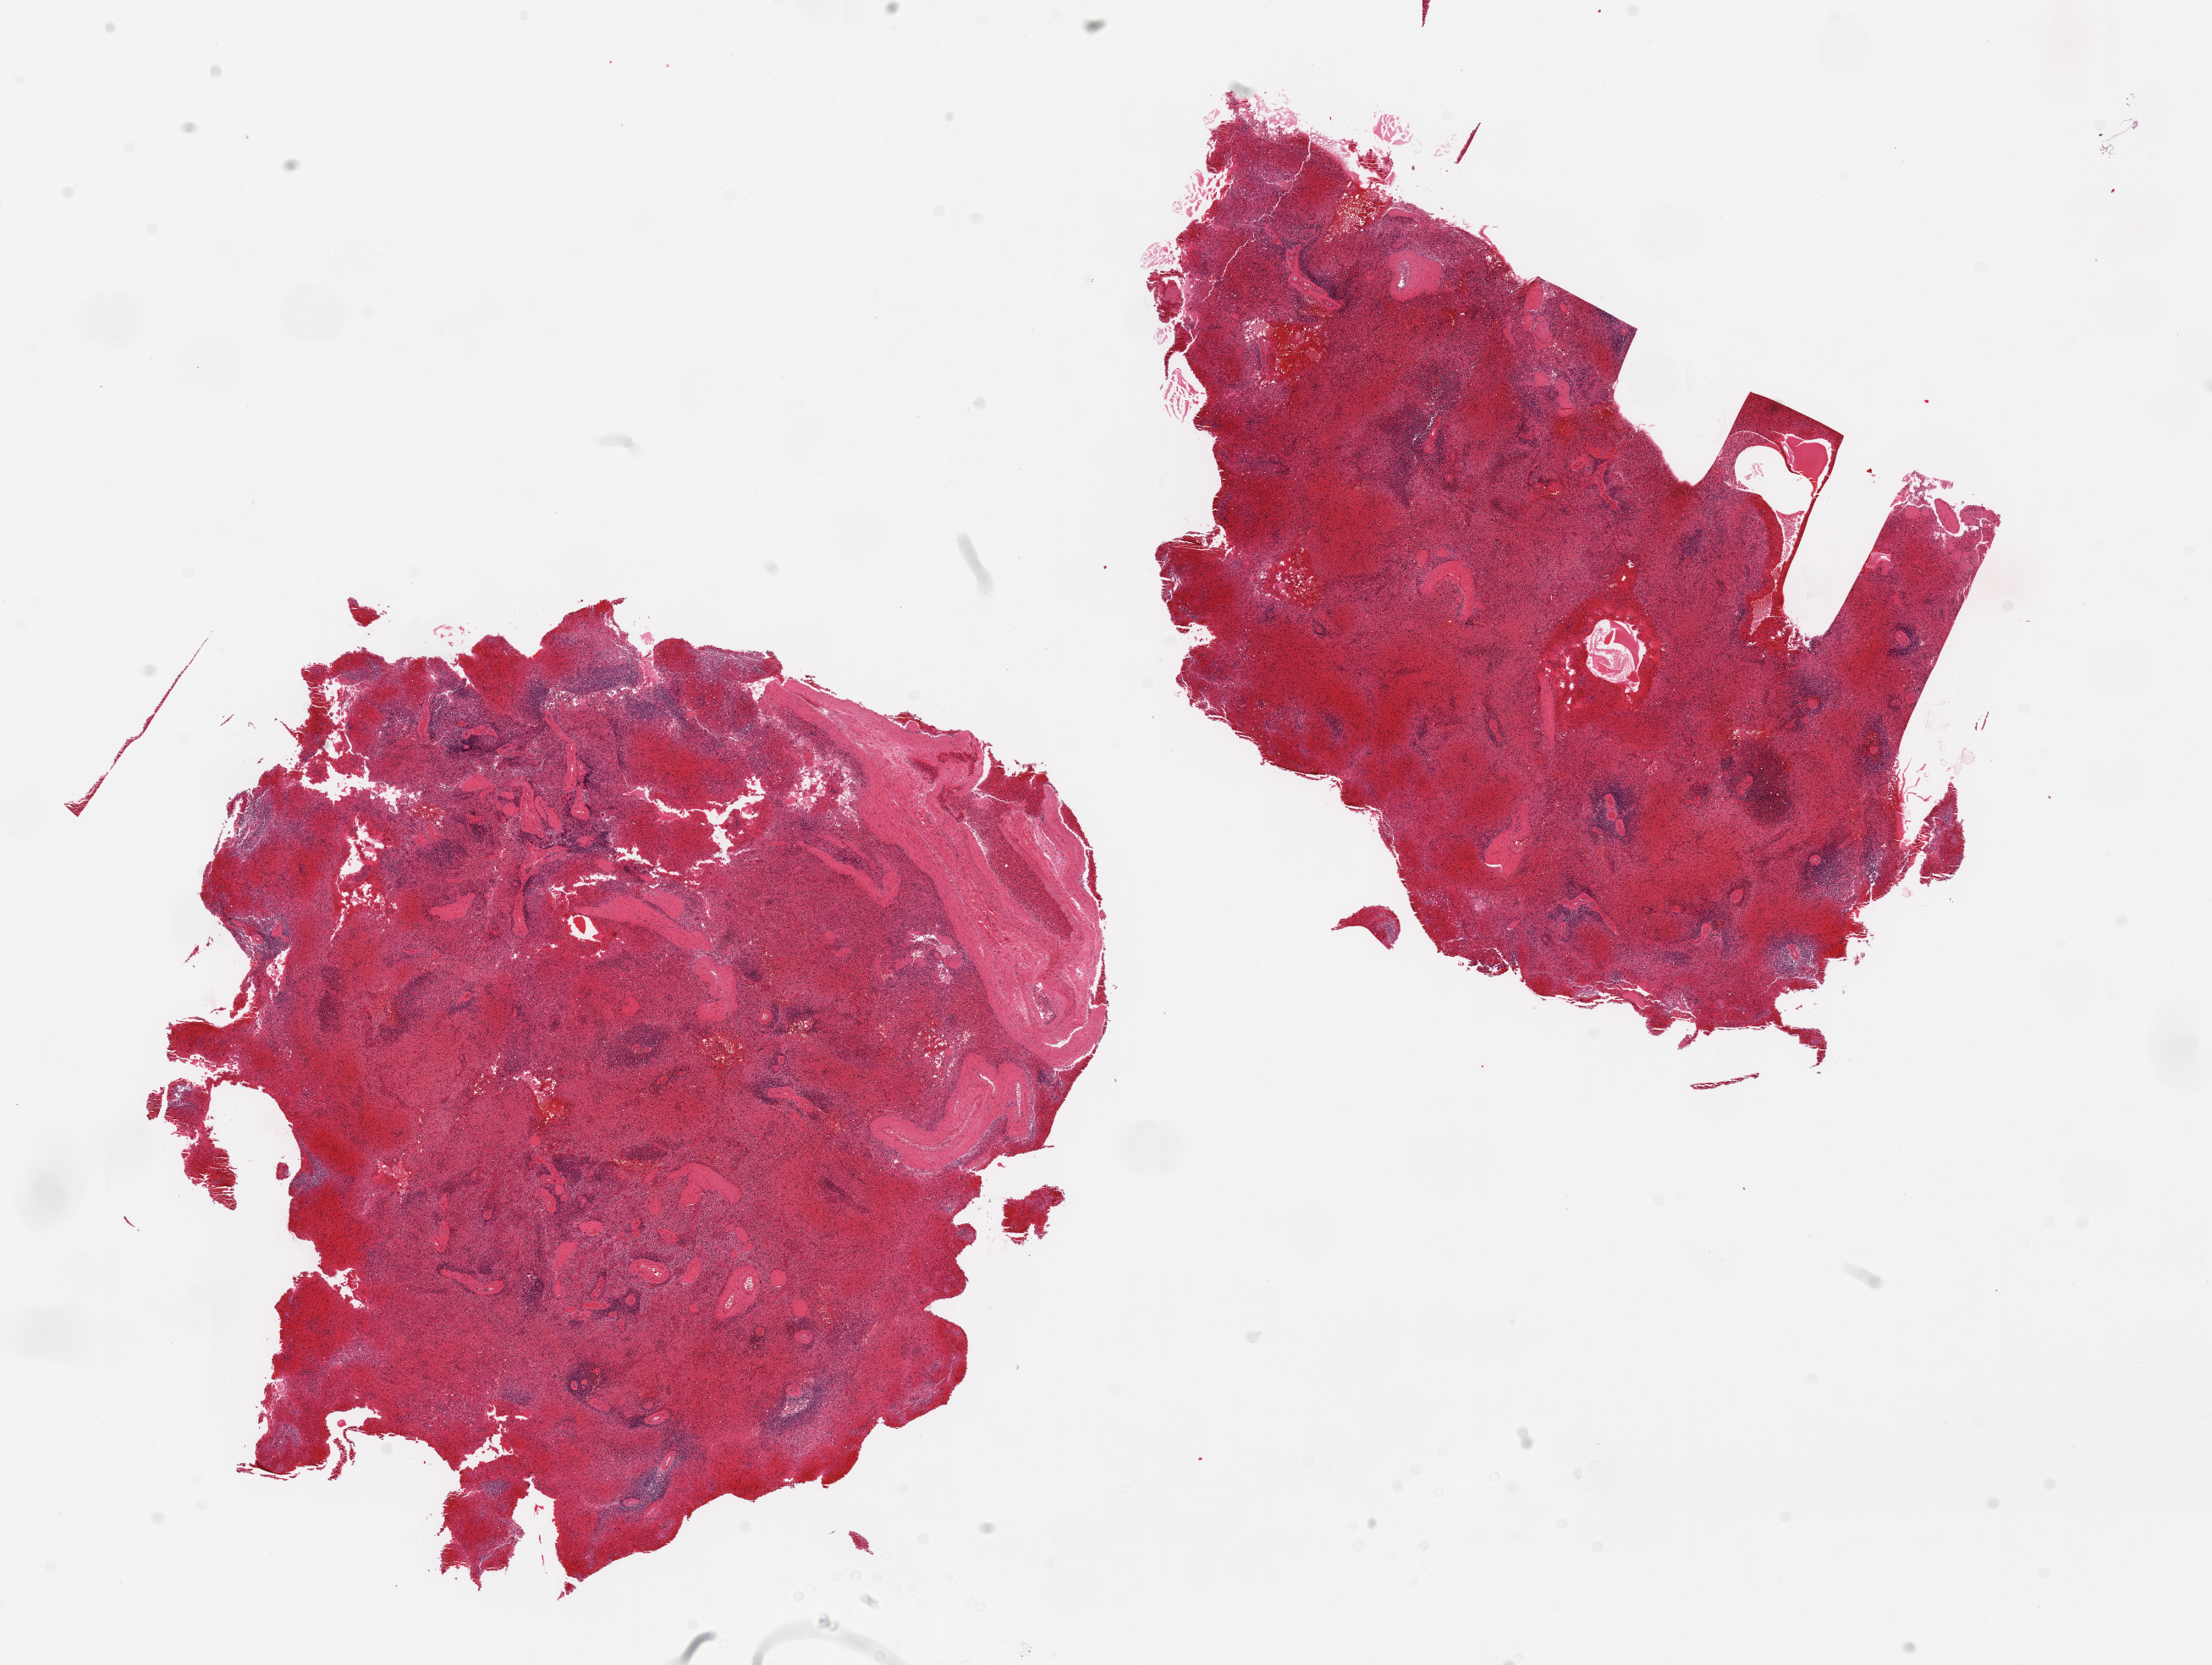
Hematoxylin and eosin (H&E) whole-slide image, brightfield, low-resolution overview of the scanned area, about 20.7 x 15.6 mm (from a 20x scan); PAXgene-fixed paraffin-embedded (PFPE) section; section of spleen (target tissue); tissue donor sample. Male donor.
• review note (as recorded): 2 pieces, congested